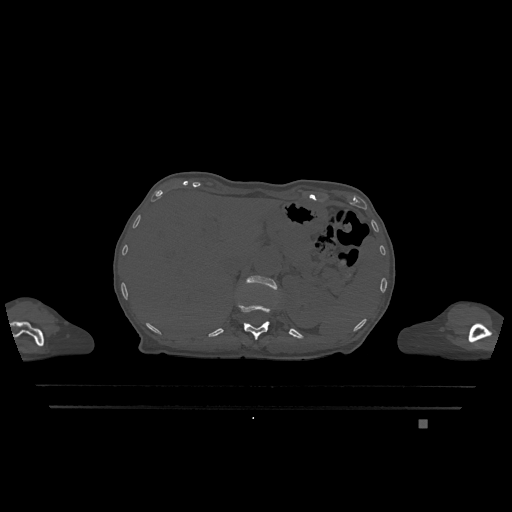
CT including the spine, one axial slice; slice 521 of 1317 in the series (ordered by position); bone window (W 1800 / L 400 HU); 0.5 mm slice thickness; 512 × 512 image matrix, field of view 500 × 500 mm. Female patient, age 74 years. From the clinical record (not read from this slice): primary cancer: lung; vertebrae with lytic lesions (as recorded): T1, T4, T5, T6, L4, L5.
Outlined on this slice (semi-automatic segmentation, software-assisted and operator-edited):
- L1 vertebra: bounding box (x1, y1, x2, y2) in pixels: (246, 275, 277, 290)
- T12 vertebra: (237, 303, 271, 340)